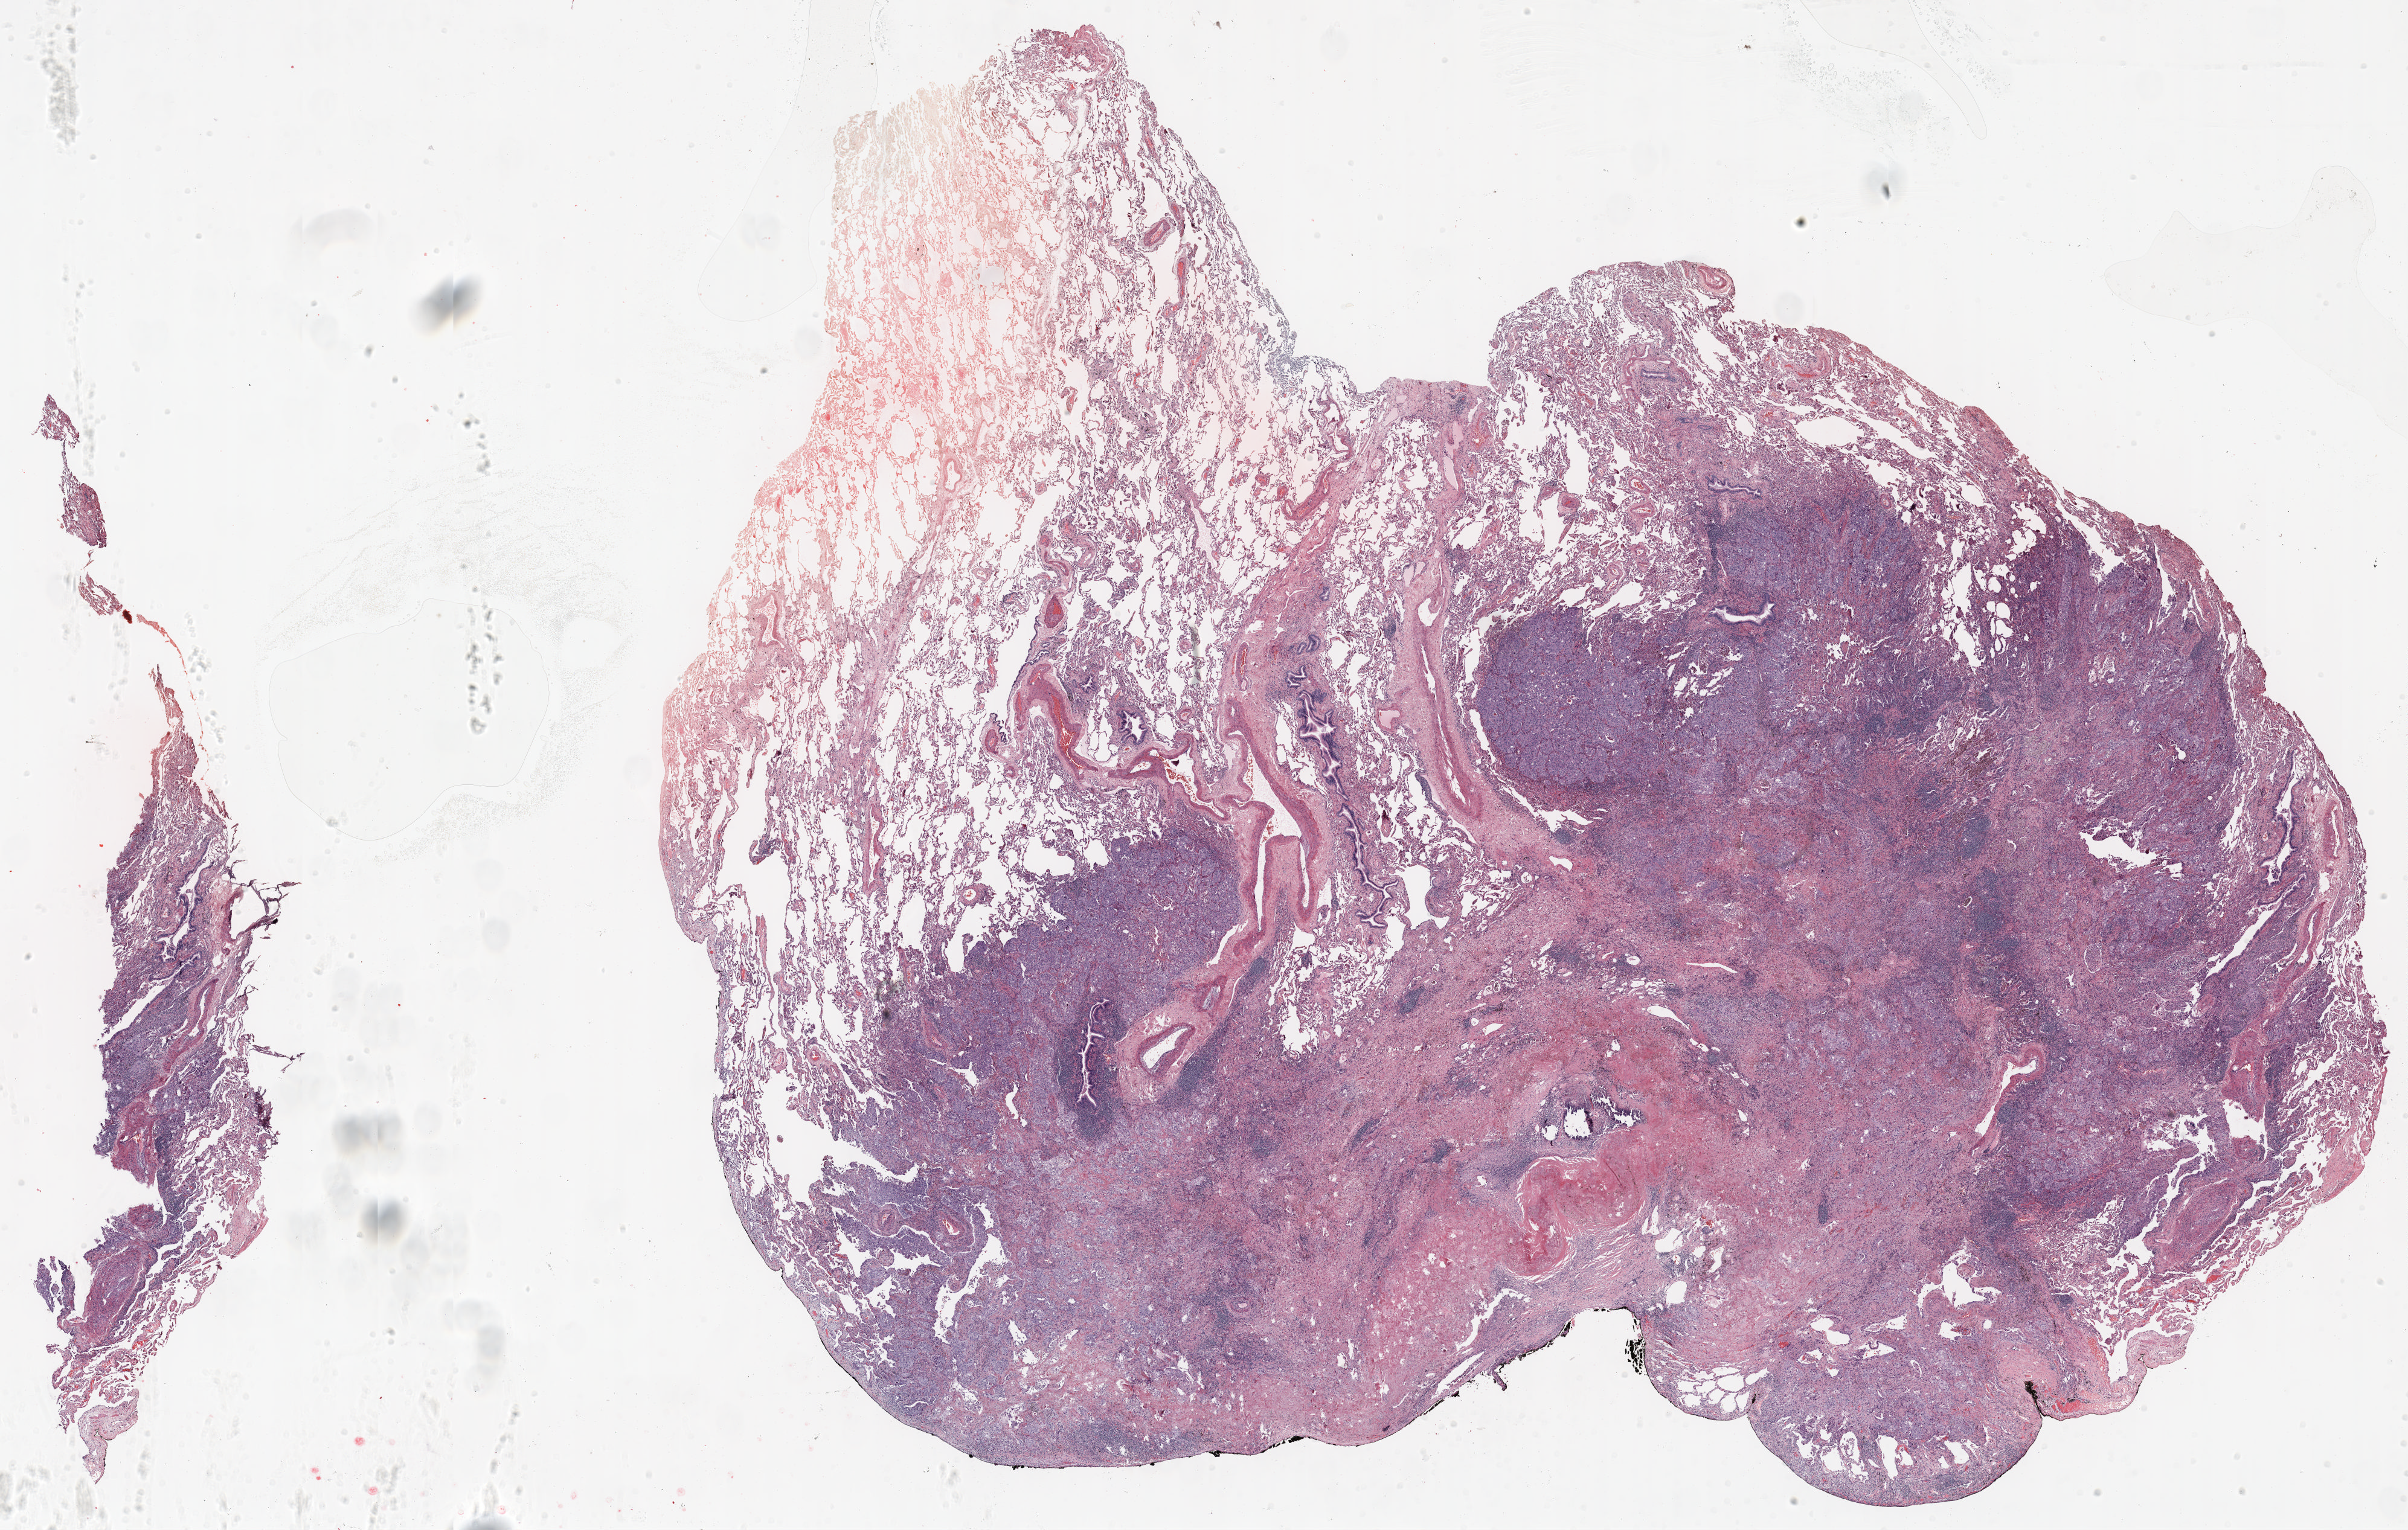
Whole-slide histology image, Hematoxylin and eosin (H&E) stained, whole scanned area (about 32.0 x 20.4 mm) shown as a low-resolution overview; FFPE section; lung tissue. Male, age 61 at enrolment. Current smoker at enrolment. Grade: poorly differentiated (G3).
Stage (AJCC 6th edition): IIIA. Primary tumour location (clinical record): left upper lobe. Participant's lung-cancer diagnosis: Adenocarcinoma, NOS. Tumour size (pathology): 30 mm.